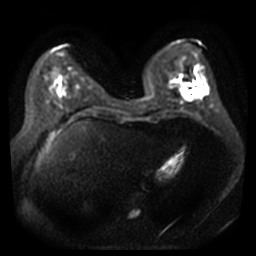
Breast MRI, one axial slice; slice 13 of 44 in the series (ordered by position); diffusion-weighted series; image 2 of 4 stored at this slice position (different b-values; order by instance number); 3 T; 5 mm slice thickness; 256 × 256 image matrix, field of view 360 × 360 mm. Female patient.
Annotated regions visible in this slice (expert manual segmentation):
- tumour on diffusion-weighted imaging: box from (x=182, y=88) to (x=191, y=101) px